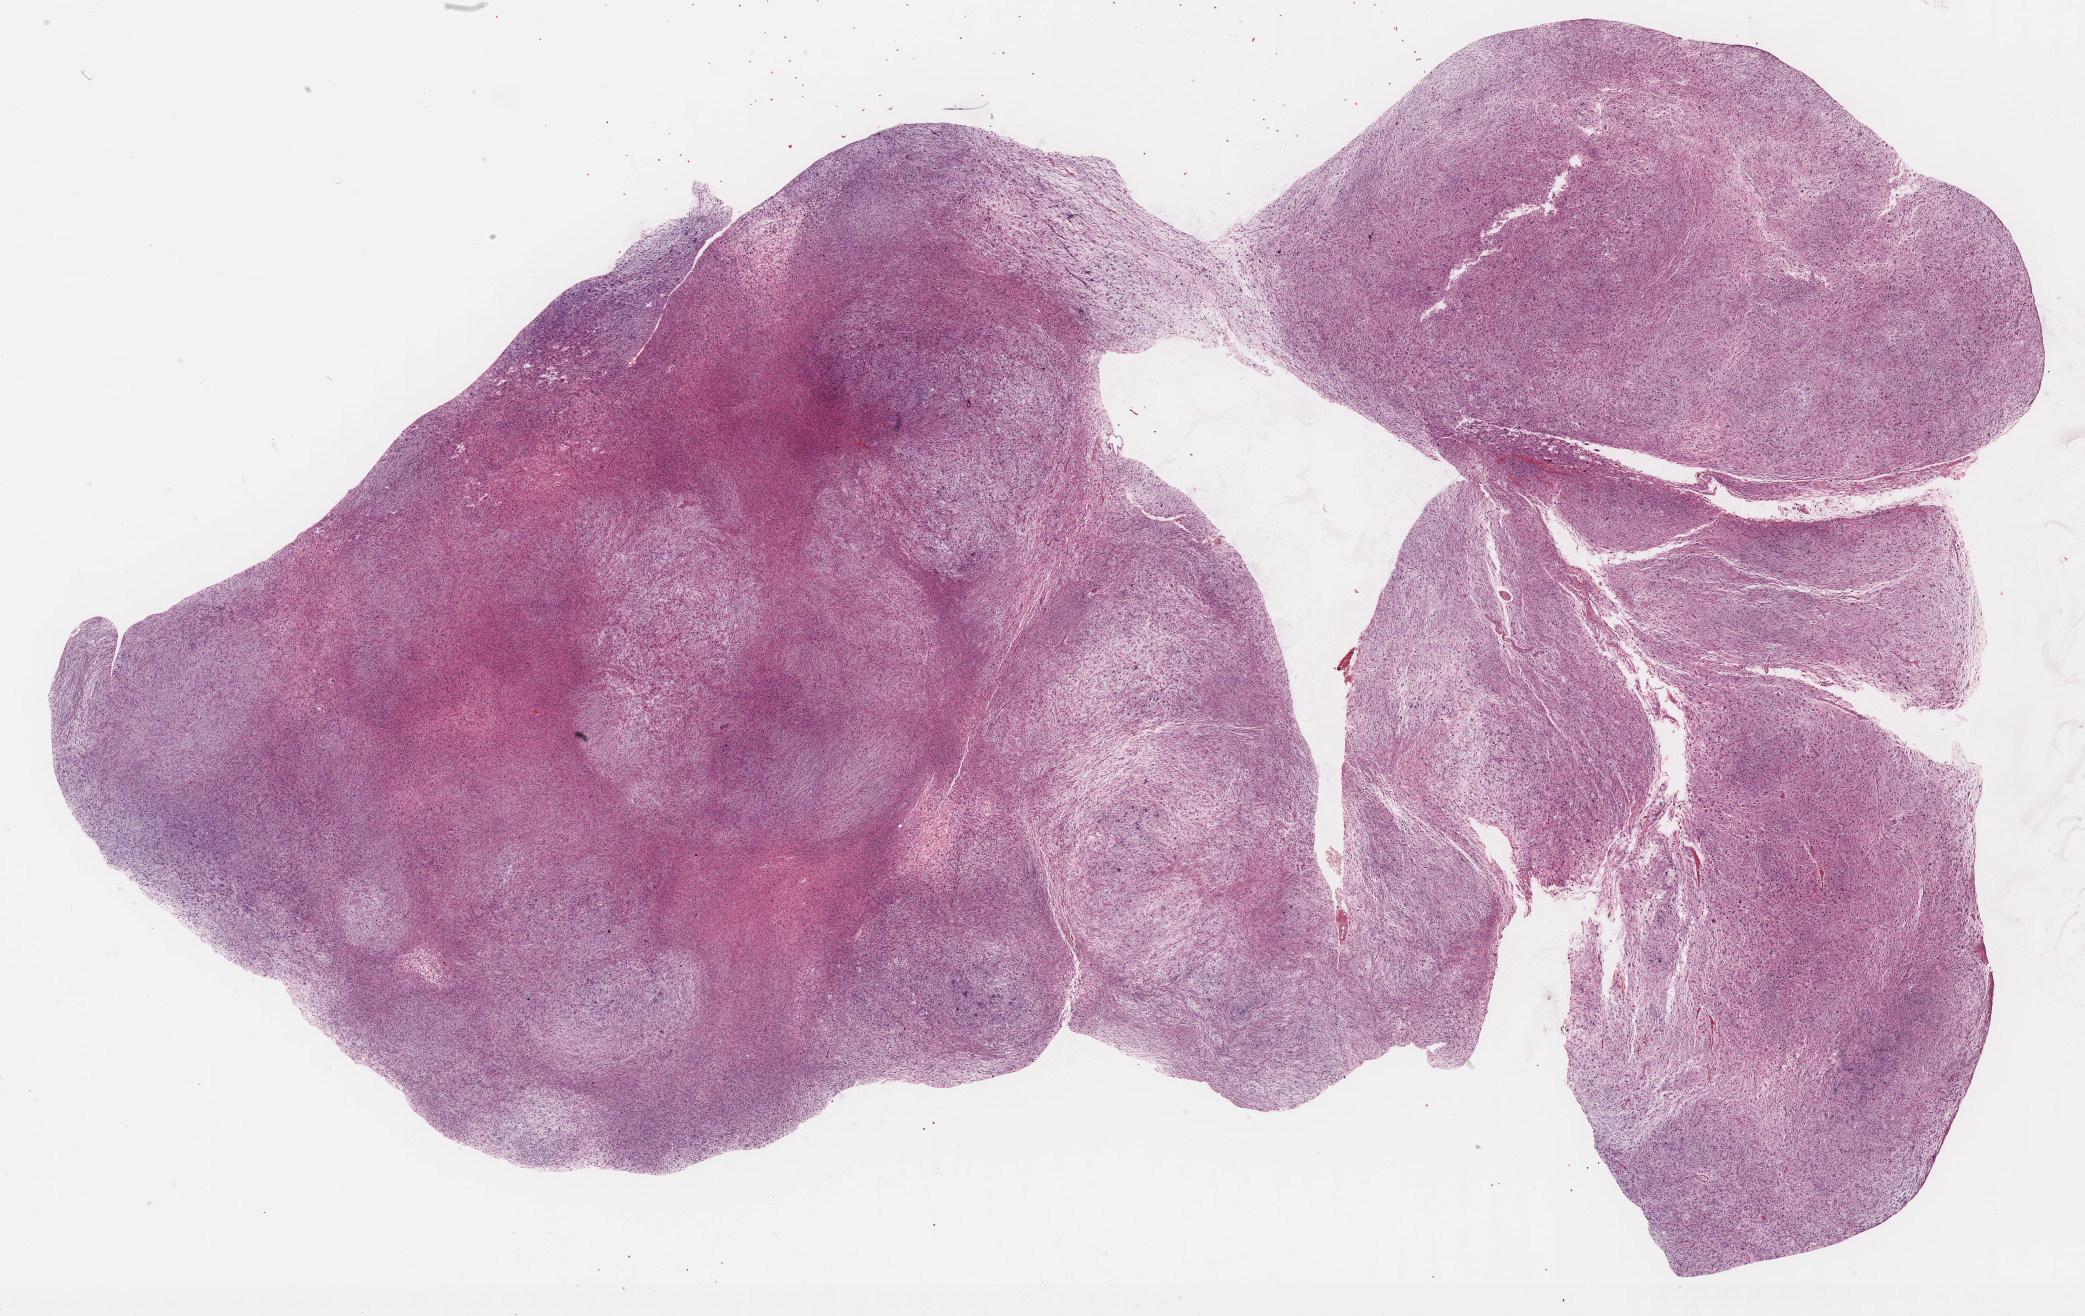
Digitized Hematoxylin and eosin (H&E) stained tissue section (whole slide) — low-resolution overview of the scanned area, about 33.7 x 21.3 mm; formalin-fixed paraffin-embedded (FFPE) diagnostic section; primary tumour sample from the connective, subcutaneous and other soft tissues. Patient sex: male.
Diagnosis: Fibromyxosarcoma (connective, subcutaneous and other soft tissues of trunk, NOS).